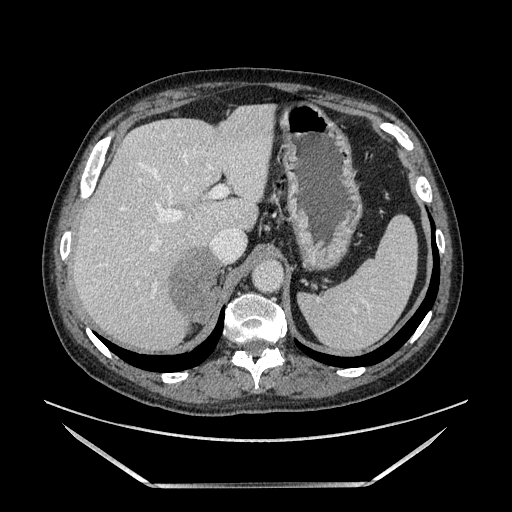
Contrast-enhanced abdominal CT, one axial slice; slice 107 of 185 in the series (ordered by position); soft-tissue window (W 400 / L 40 HU); 1.25 mm slice thickness; 512 × 512 image matrix, field of view 440 × 440 mm. Male patient. Case-level facts recorded for this patient, not image findings: diagnosis: adrenocortical carcinoma; tumour side: right adrenal; tumour size at pathology: 10.3 cm; Ki-67 index: 20 %; stage (as recorded): 3.
Structures marked on this image (semi-automatic segmentation, software-assisted and operator-edited):
- mass: bounding box <171,247,221,324> (left, top, right, bottom; pixels)